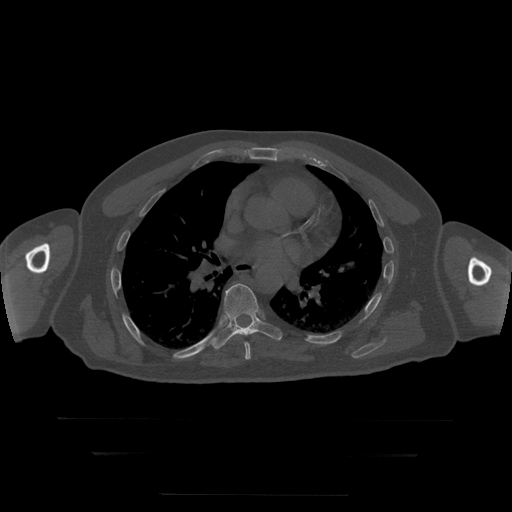
CT including the spine, one axial slice. Slice 171 of 397 in the series (ordered by position). Bone window (W 1800 / L 400 HU). 1.25 mm slice thickness. 512 × 512 image matrix, field of view 510 × 510 mm. Patient age 73 years. From the clinical record (not read from this slice): primary cancer: prostate.
Annotated regions visible in this slice (semi-automatic segmentation, software-assisted and operator-edited):
- T7 vertebra: box from (x=245, y=342) to (x=251, y=360) px
- T8 vertebra: (x=211, y=284)–(x=283, y=350)